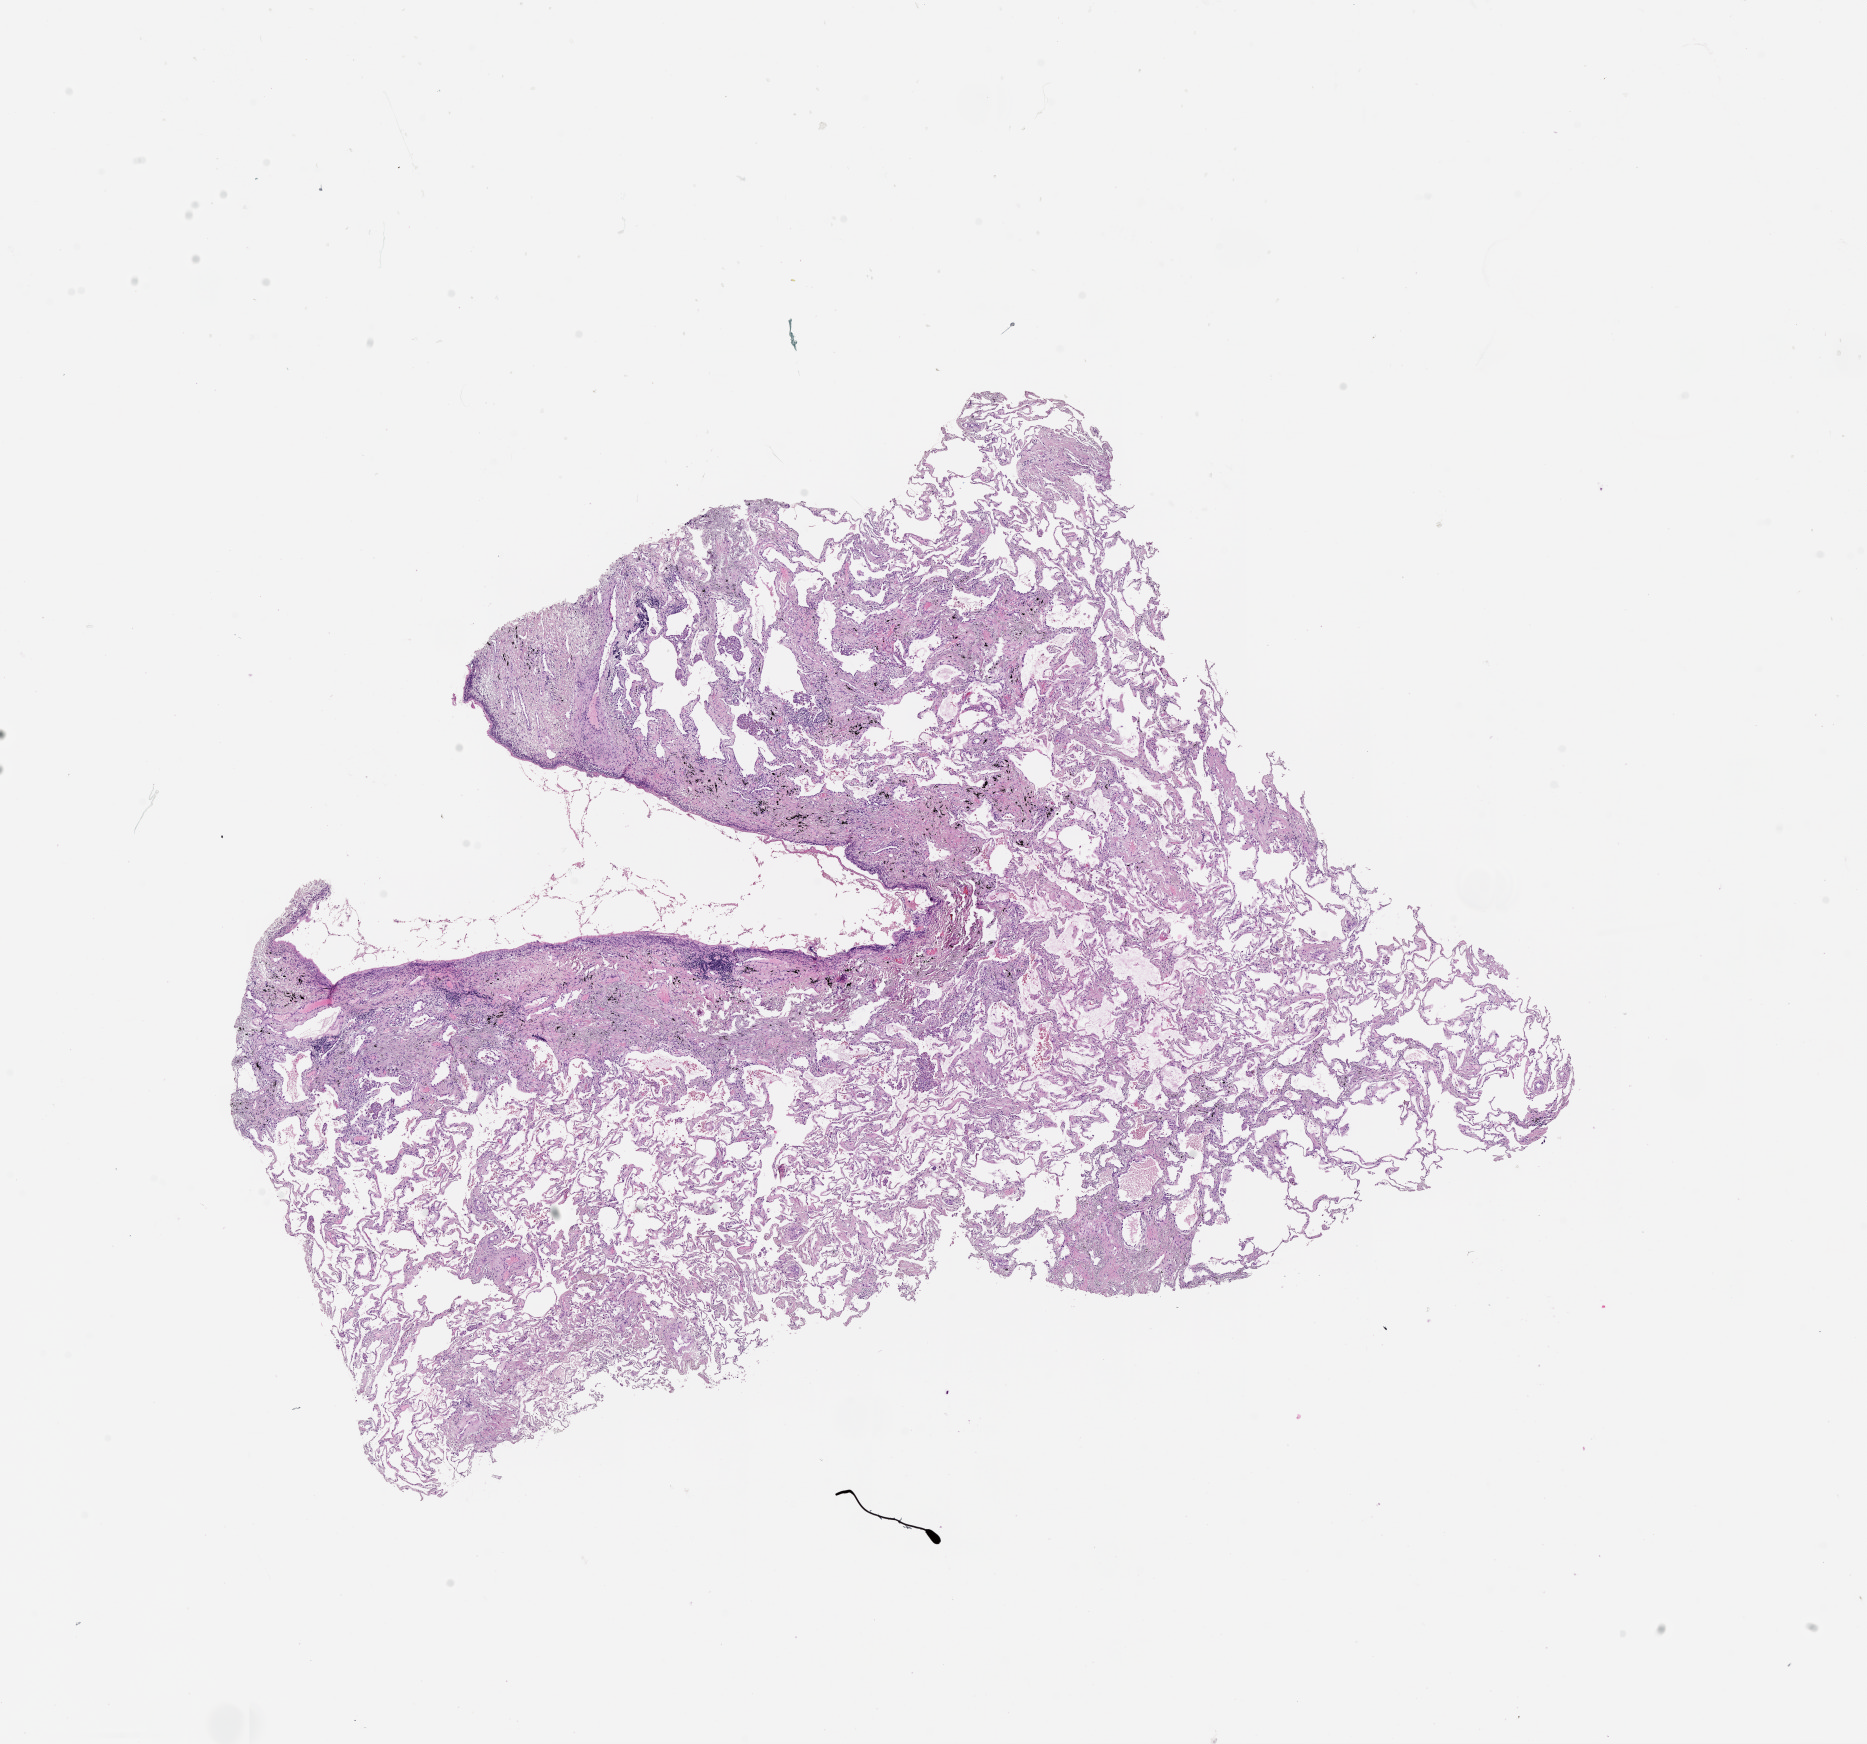
Digitized Hematoxylin and eosin (H&E) stained tissue section (whole slide) — a low-resolution overview of the entire scanned area, about 15.0 x 14.0 mm (from a 20x scan); lung, normal (non-tumour) tissue. 77-year-old male patient.
This section: normal (non-tumour) tissue from the same patient. Patient diagnosis (cohort enrolment): squamous cell carcinoma (lung).